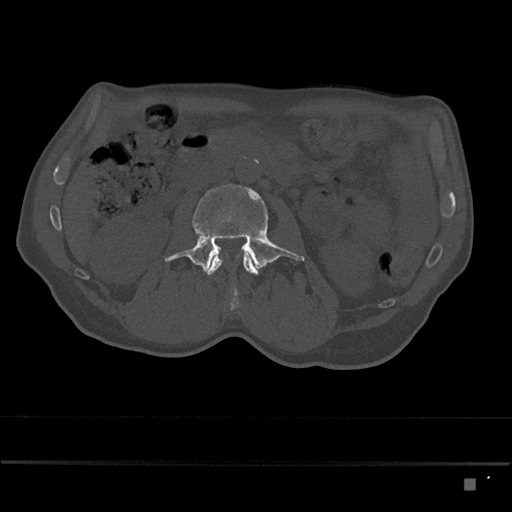
CT including the spine, one axial slice; reconstruction kernel Br40s/3; bone window (W 1800 / L 400 HU); 0.5 mm slice thickness; 512 × 512 image matrix. Male patient, age 72 years. From the clinical record (not read from this slice): primary cancer: prostate.
Structures marked on this image (semi-automatic segmentation, software-assisted and operator-edited):
- L2 vertebra: bounding box <203,253,258,289> (left, top, right, bottom; pixels)
- L3 vertebra: <165,184,305,290>